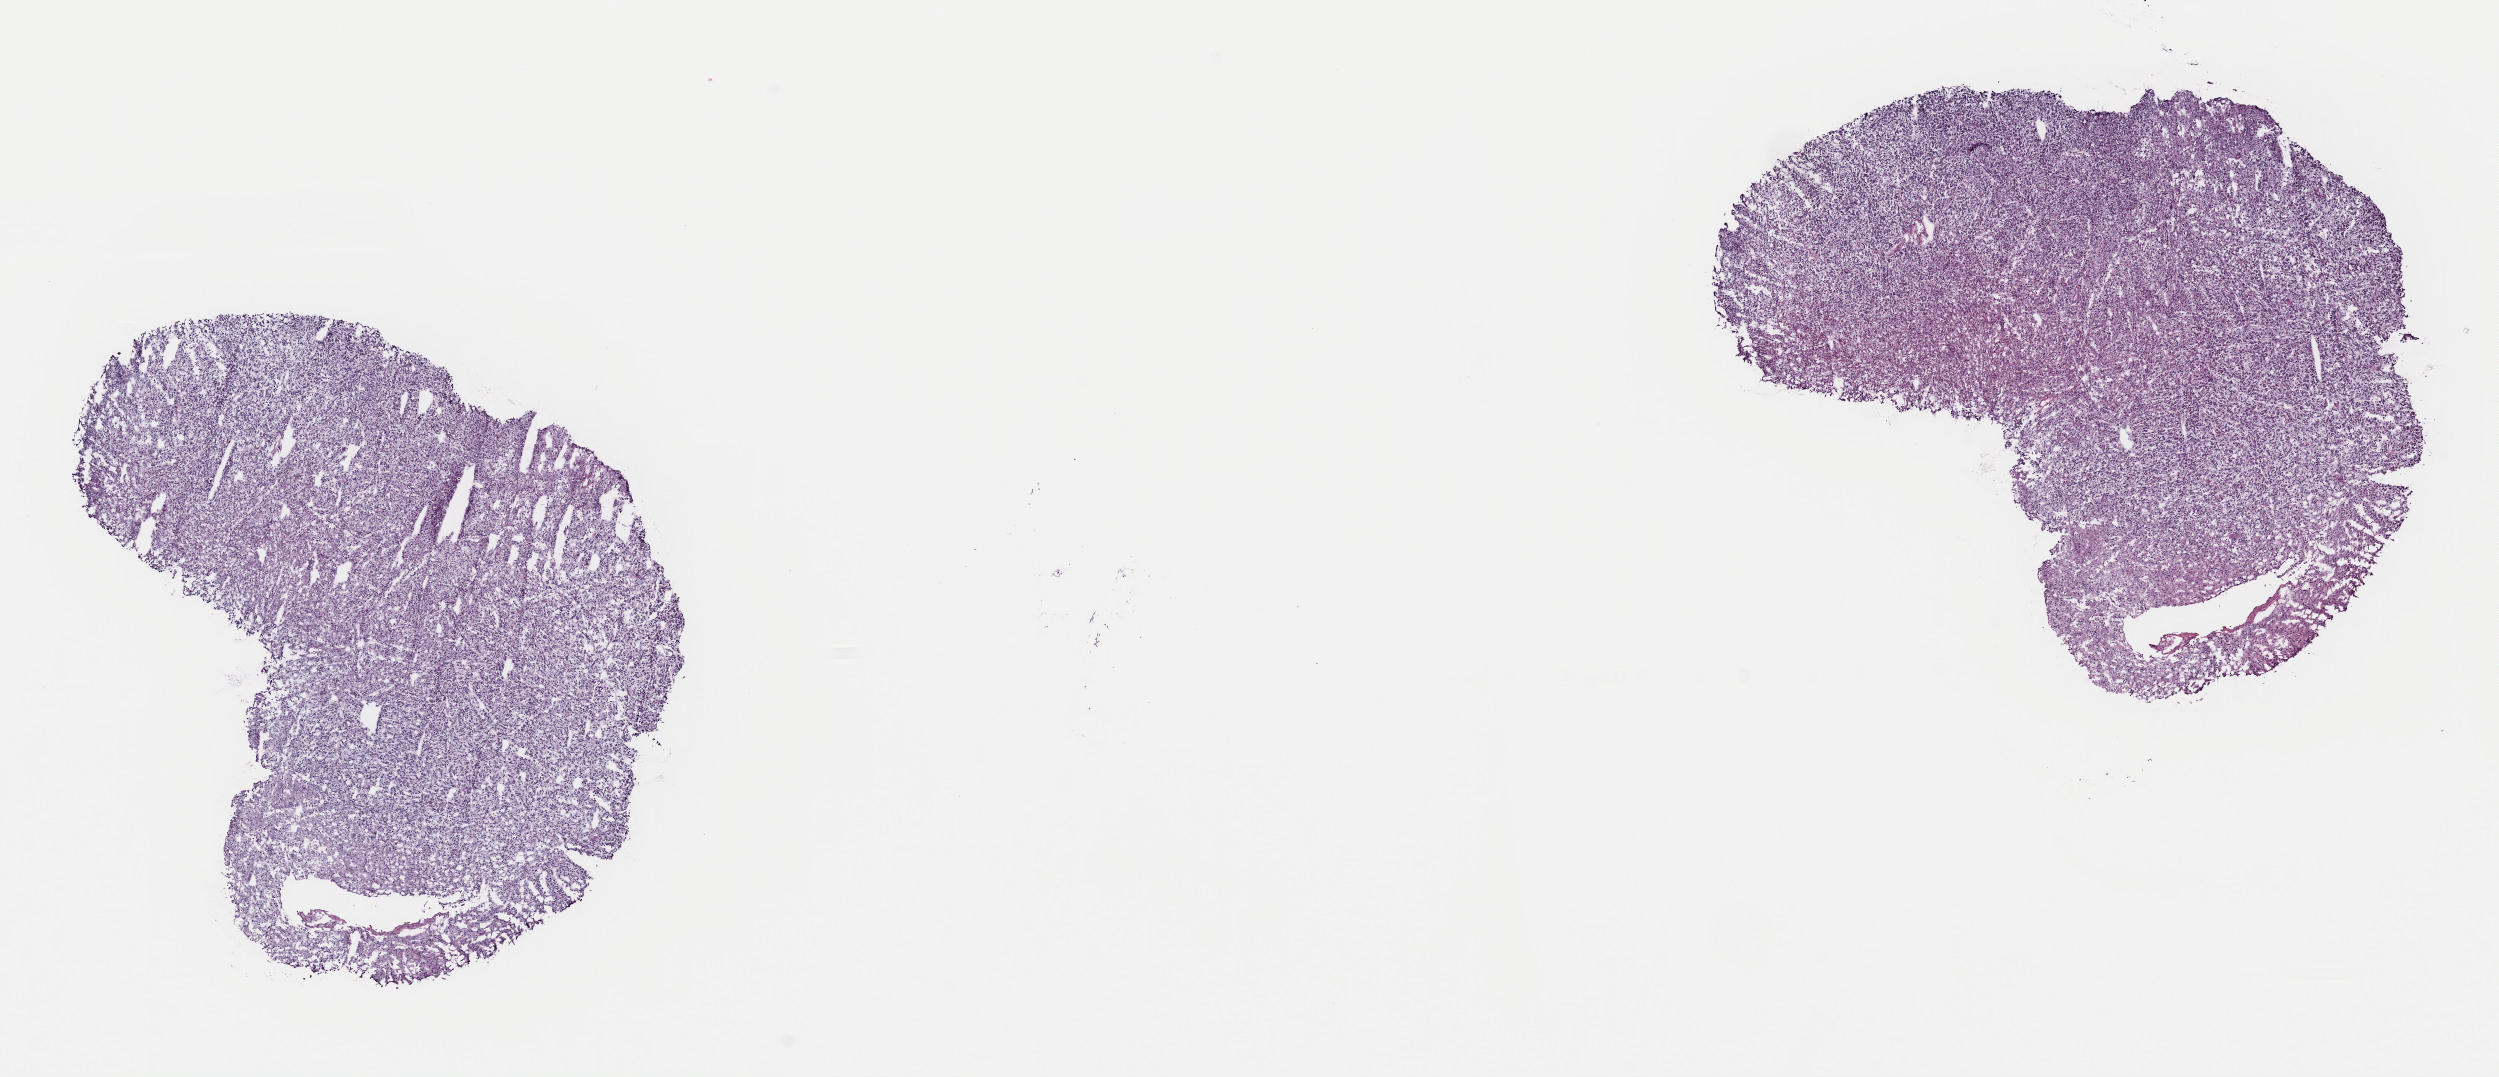
Whole-slide histology image, H&E-stained — low-resolution overview of the scanned area, about 19.7 x 8.5 mm, frozen section from the top of the tissue portion, brain, primary tumour sample. Male, age 70 years at initial diagnosis. Histologic grade: G3 (poorly differentiated). Pathologist review of this section (percent, as recorded): tumour cells 90%, tumour nuclei 90%, normal cells 5%, stromal cells 5%, necrosis 0%. Infiltration values recorded for this section: lymphocyte infiltration 0%, monocyte infiltration 0%, neutrophil infiltration 0%.
- diagnosis: Oligodendroglioma, anaplastic (cerebrum)